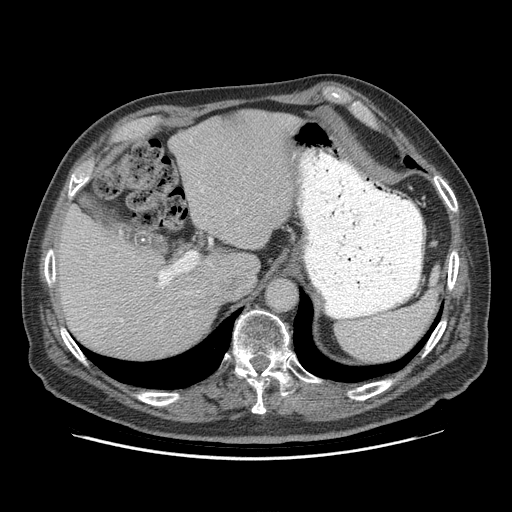
Contrast-enhanced abdominal CT (liver protocol), one axial slice. Position 66 of 95 along the scan axis. 140 kVp. Soft-tissue window (W 400 / L 40 HU). 2.5 mm slice thickness. 512 × 512 image matrix, field of view 400 × 400 mm. Case-level facts recorded for this patient, not image findings: diagnosis: hepatocellular carcinoma (patient treated with transarterial chemoembolisation; whether this scan precedes or follows treatment is not stated here); TNM stage (as recorded): Stage-IVB; Child-Pugh class: A; tumour nodularity: uninodular.
Annotated regions visible in this slice (semi-automatically segmented with operator editing):
- abdominal aorta: bounding box <267,279,297,310> (left, top, right, bottom; pixels)
- liver parenchyma outside the tumour (the mass and vessels are separate outlines, so this box may not span the whole liver): <54,110,300,358>
- liver vessels: <159,260,196,286>